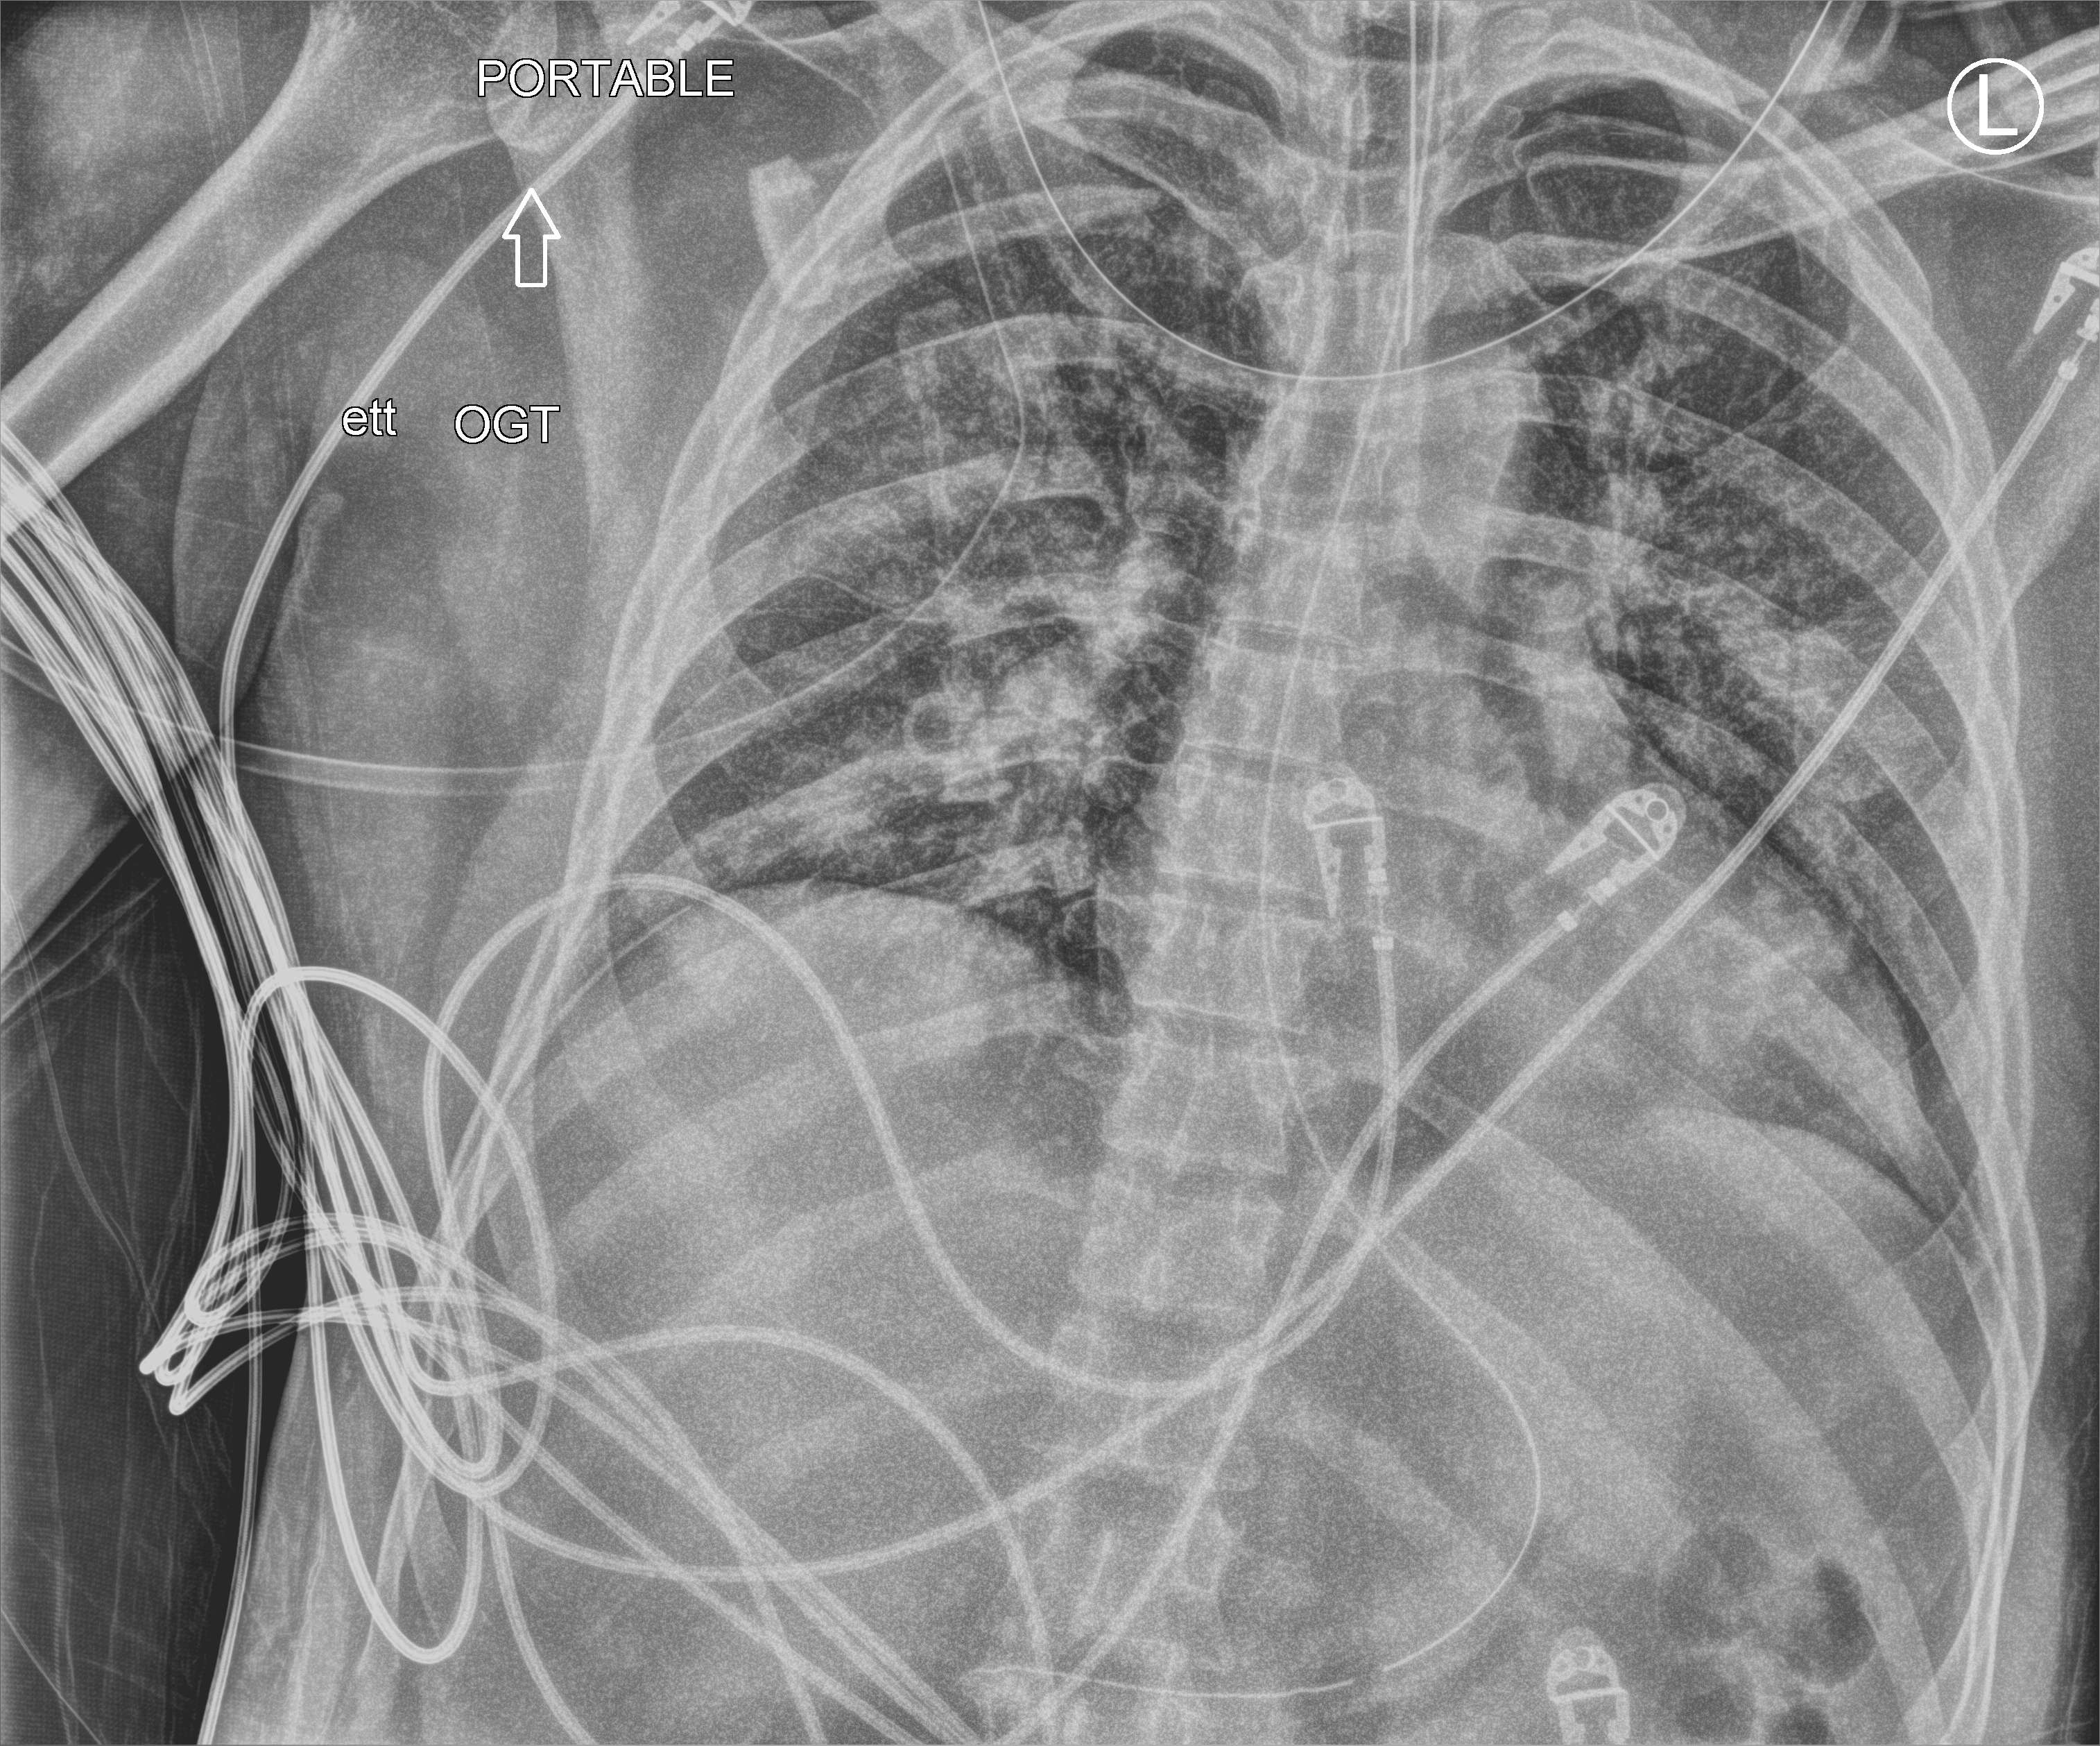
Bedside chest radiograph (computed radiography), anteroposterior (AP) projection. Patient hospitalised with COVID-19; male, aged 18–59 years.
Hospital-stay facts (about this admission, not read from this image; timing relative to this image not recorded):
- admitted to intensive care during this hospital stay: yes
- hypertension (admission record): no
- length of hospital stay: 31 days